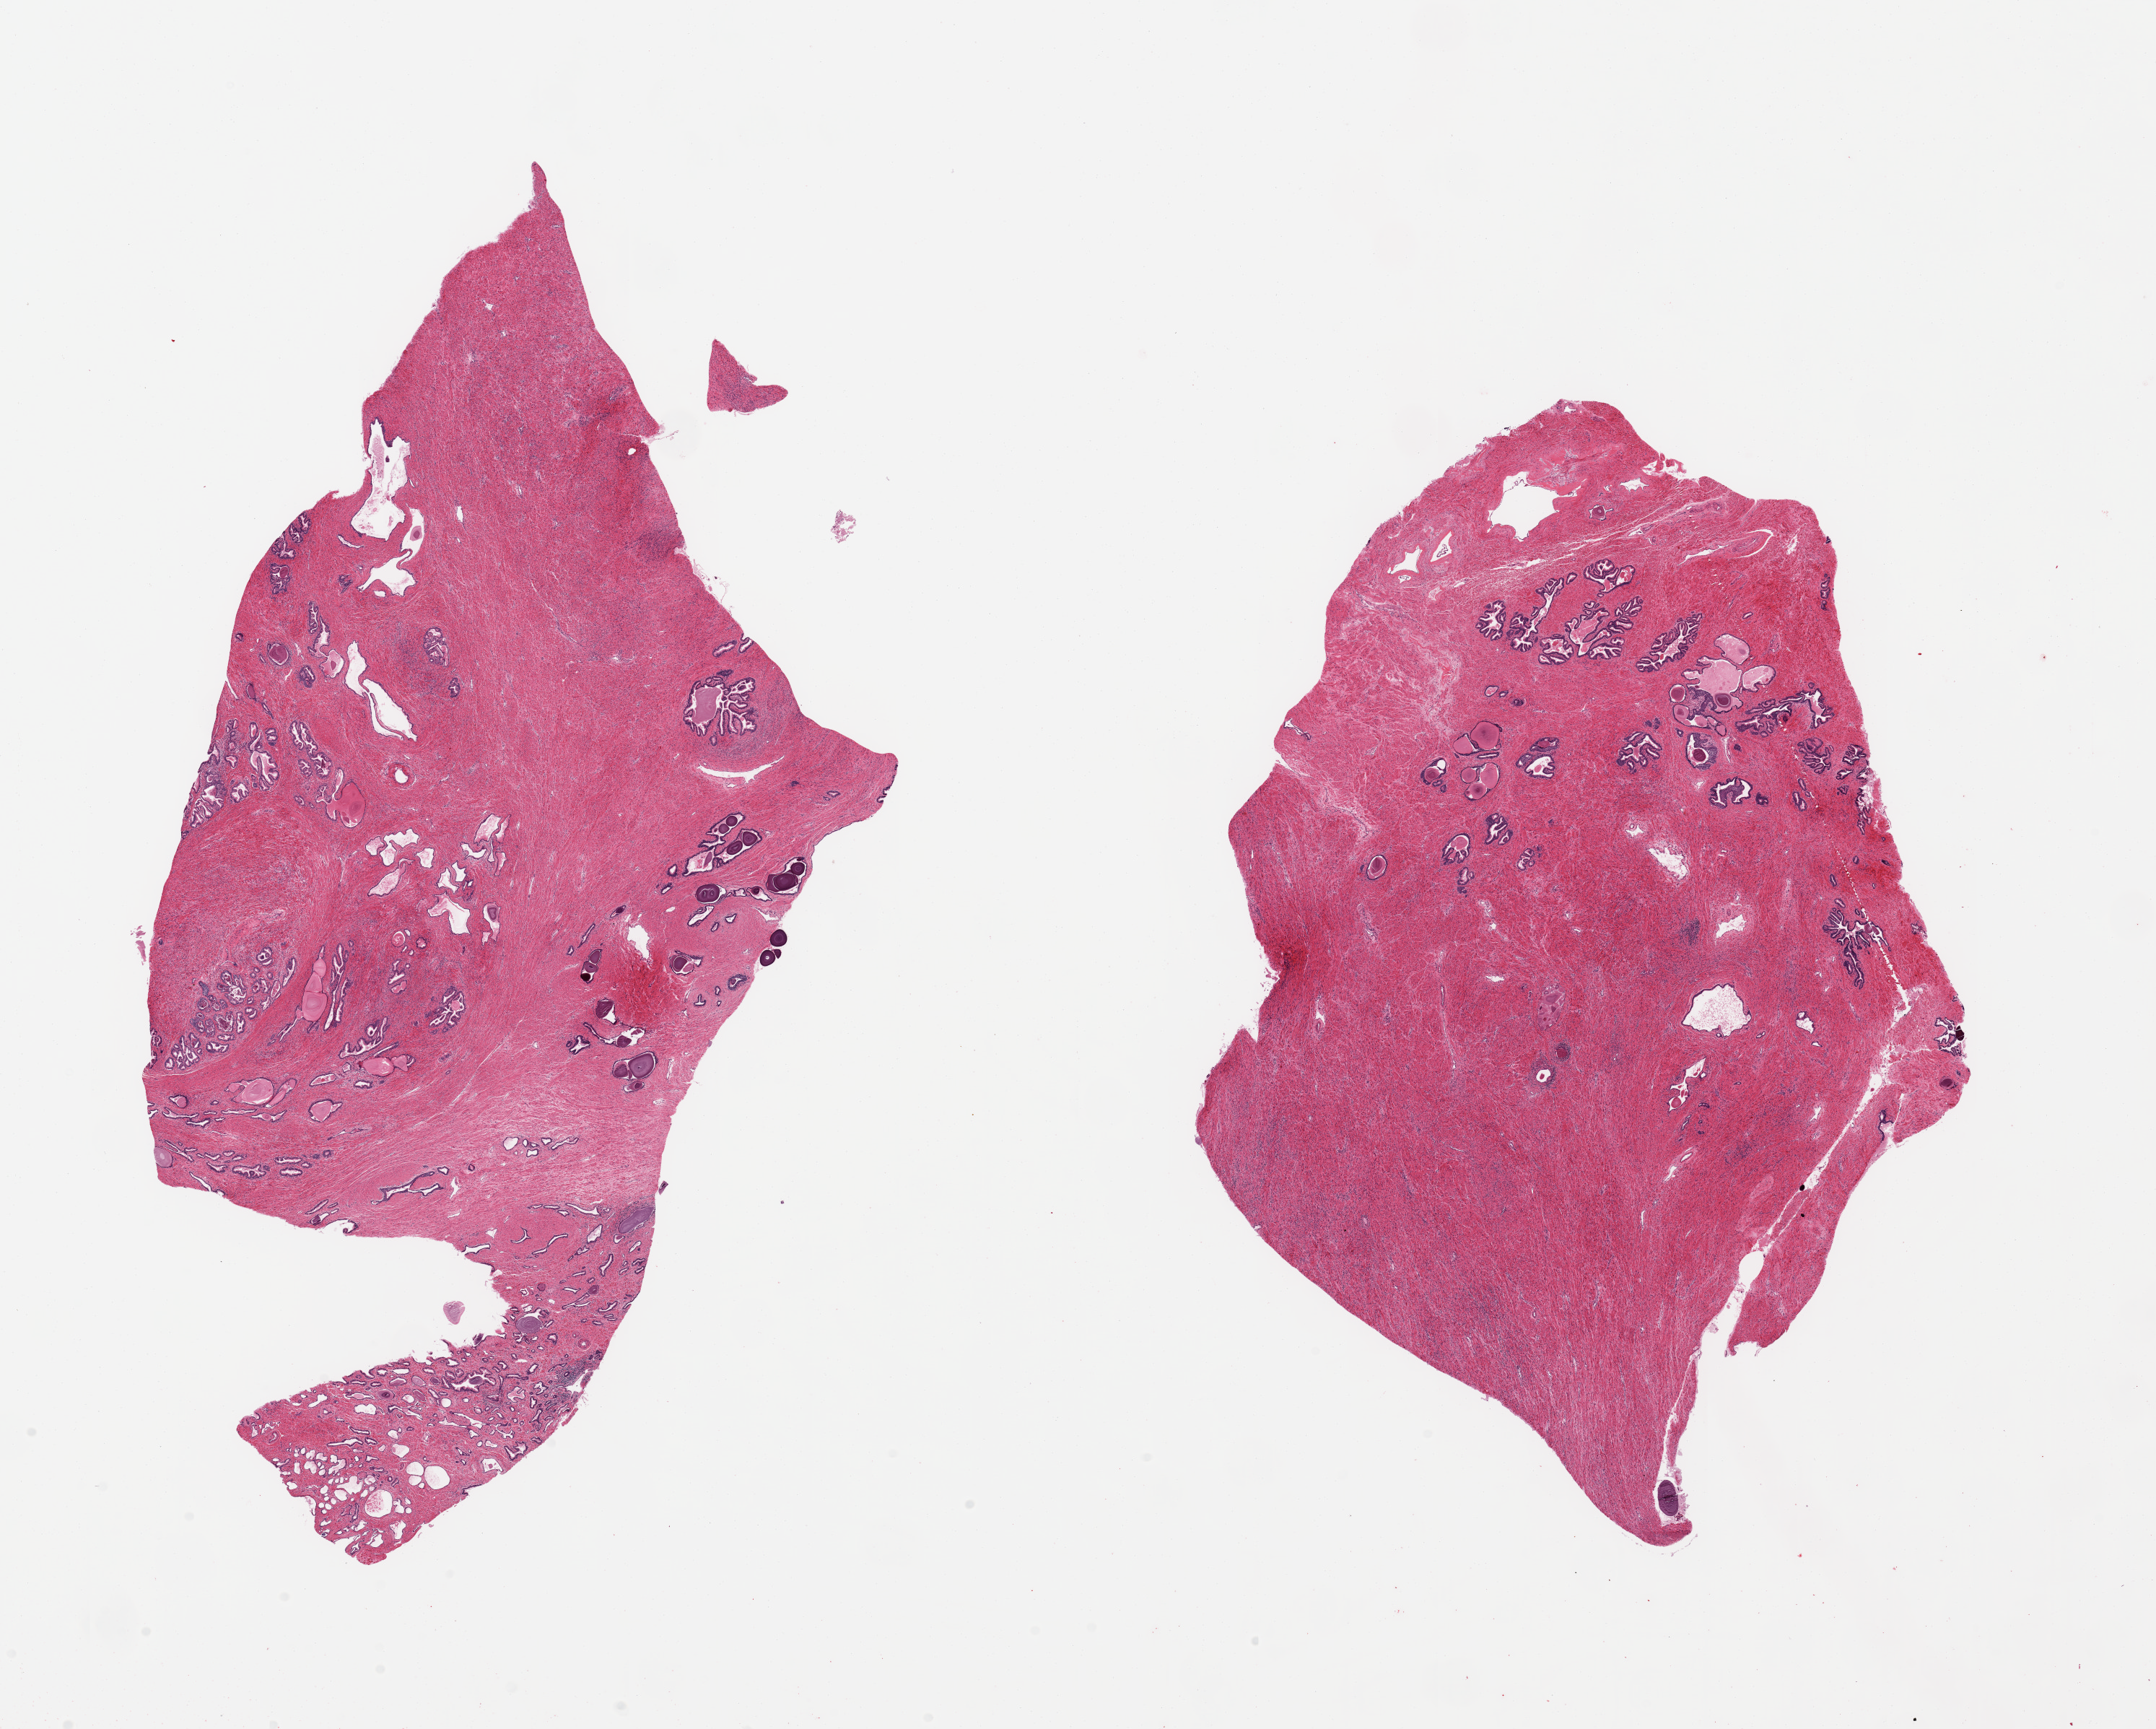
Digitized hematoxylin and eosin (H&E)-stained section — whole scanned area (about 23.6 x 18.9 mm, slide scanned at 20x) shown as a low-resolution overview; PAXgene-fixed, paraffin-embedded tissue; target tissue: prostate; donor tissue sample. Donor: male.
- review note (as recorded): 2 pieces; focal chronic inflammation and atrophy